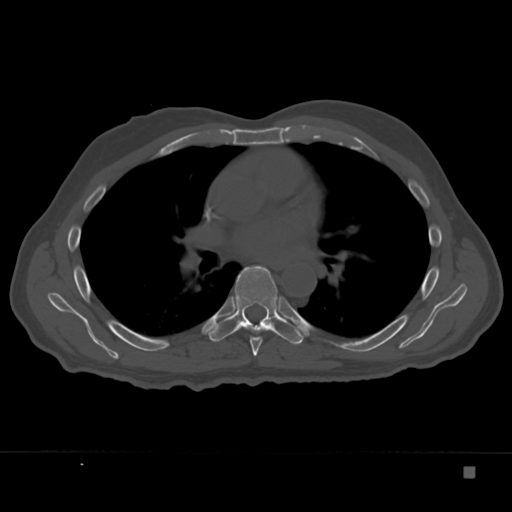
CT including the spine, one axial slice; slice 229 of 332 in the series (ordered by position); bone window (W 1800 / L 400 HU); 512 × 512 image matrix. Patient: male, 72 years. Case-level facts recorded for this patient, not image findings: primary cancer: skeletal.
Structures marked on this image (semi-automatic segmentation, software-assisted and operator-edited):
- T6 vertebra: box from (x=250, y=337) to (x=262, y=356) px
- T7 vertebra: (x=209, y=265)–(x=306, y=345)